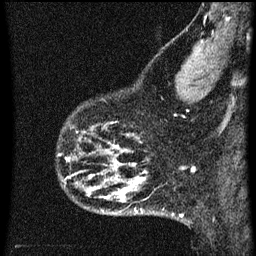
Breast MRI (dynamic contrast-enhanced), one sagittal slice; position 13 of 60 along the scan axis; dynamic contrast-enhanced series, image 2 of 3 at this slice position (ordered by acquisition); 1.5 T; TE 4.2 ms, TR 8 ms; 2 mm slice thickness; 256 × 256 image matrix, field of view 180 × 180 mm. Patient: female, 43 years.
Outlined on this slice (semi-automatically segmented with operator editing):
- analysis volume of interest (the breast-tissue region the enhancement analysis was run in; not a lesion): bounding box (x1, y1, x2, y2) in pixels: (58, 104, 104, 153)
- tumour enhancement mask (voxels above the 70 % enhancement threshold inside the analysis volume of interest): (79, 128, 92, 141)